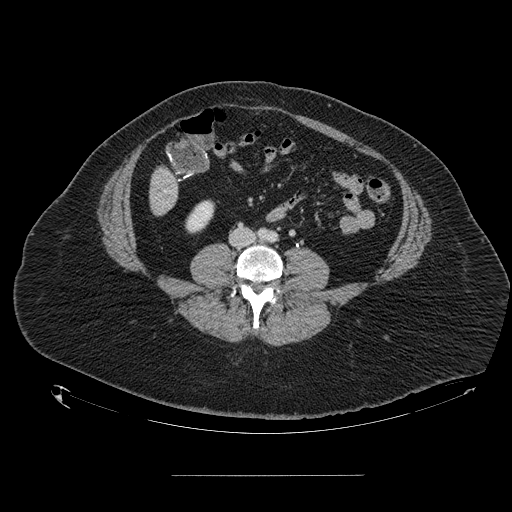
Contrast-enhanced abdominal CT, one axial slice; slice 15 of 164 in the series (ordered by position); 120 kVp; intravenous contrast given; soft-tissue window (W 400 / L 40 HU); 2.5 mm slice thickness; 512 × 512 image matrix, field of view 495 × 495 mm. Female patient, age 52 years. From the clinical record (not read from this slice): diagnosis: colorectal cancer liver metastases, imaged before liver resection; multiple liver metastases: yes; largest metastasis: 3.5 cm; disease in both lobes: no.
Structures marked on this image (expert manual segmentation):
- liver: box from (x=150, y=168) to (x=178, y=214) px